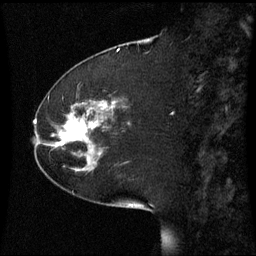
Breast MRI (dynamic contrast-enhanced), one sagittal slice; slice 20 of 60 in the series (ordered by position); dynamic contrast-enhanced series, image 2 of 3 at this slice position (ordered by acquisition); 1.5 T; TE 4.2 ms, TR 8.9 ms; 256 × 256 image matrix, field of view 220 × 220 mm. Female patient, age 51 years. Case-level facts recorded for this patient, not image findings: setting: breast cancer imaged before/during neoadjuvant chemotherapy; receptor status: HR-positive, HER2-negative.
Annotated regions visible in this slice (semi-automatically segmented with operator editing):
- analysis volume of interest (the breast-tissue region the enhancement analysis was run in; not a lesion): bounding box (x1, y1, x2, y2) in pixels: (44, 102, 109, 169)
- tumour enhancement mask (voxels above the 70 % enhancement threshold inside the analysis volume of interest): (58, 120, 95, 147)